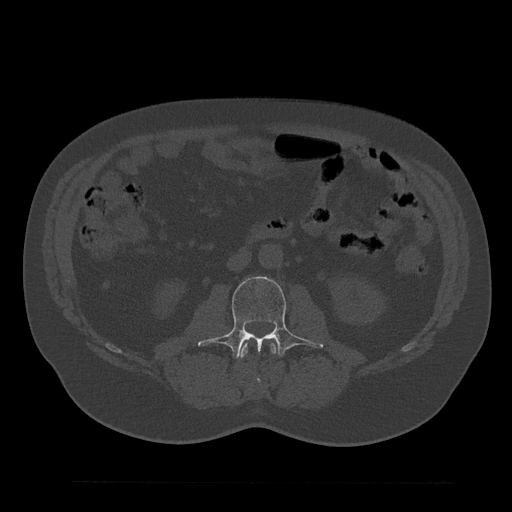
CT including the spine, one axial slice; slice 47 of 797 in the series (ordered by position); 120 kVp; bone window (W 1800 / L 400 HU); 0.5 mm slice thickness; 512 × 512 image matrix, field of view 430 × 430 mm. Male patient, age 61 years. From the clinical record (not read from this slice): primary cancer: prostate.
Annotated regions visible in this slice (semi-automatic segmentation, software-assisted and operator-edited):
- L2 vertebra: bounding box <239,343,277,385> (left, top, right, bottom; pixels)
- L3 vertebra: <198,276,323,359>